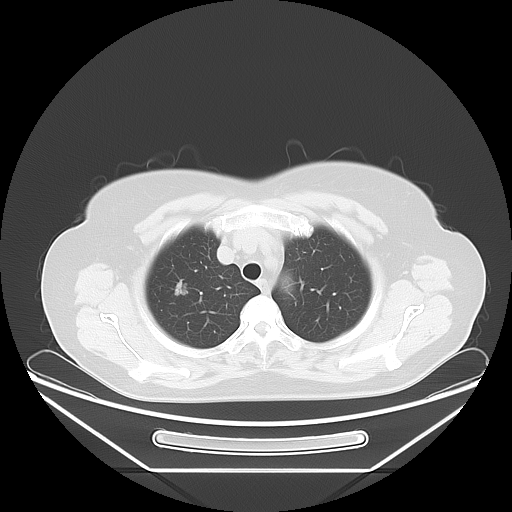
Chest CT, one axial slice; position 50 of 59 along the scan axis; reconstruction kernel LUNG; 120 kVp; lung window (W 1500 / L -600 HU); 5 mm slice thickness; 512 × 512 image matrix. Female patient, age 60 years. Case-level facts recorded for this patient, not image findings: clinical TNM (as recorded): T1c N0 M0; histopathological grade: G2-3.
Outlined on this slice (rectangle marked by the reading radiologist):
- lung tumour (recorded histology: adenocarcinoma): bounding box [x1, y1, x2, y2] px = [169, 277, 194, 307]